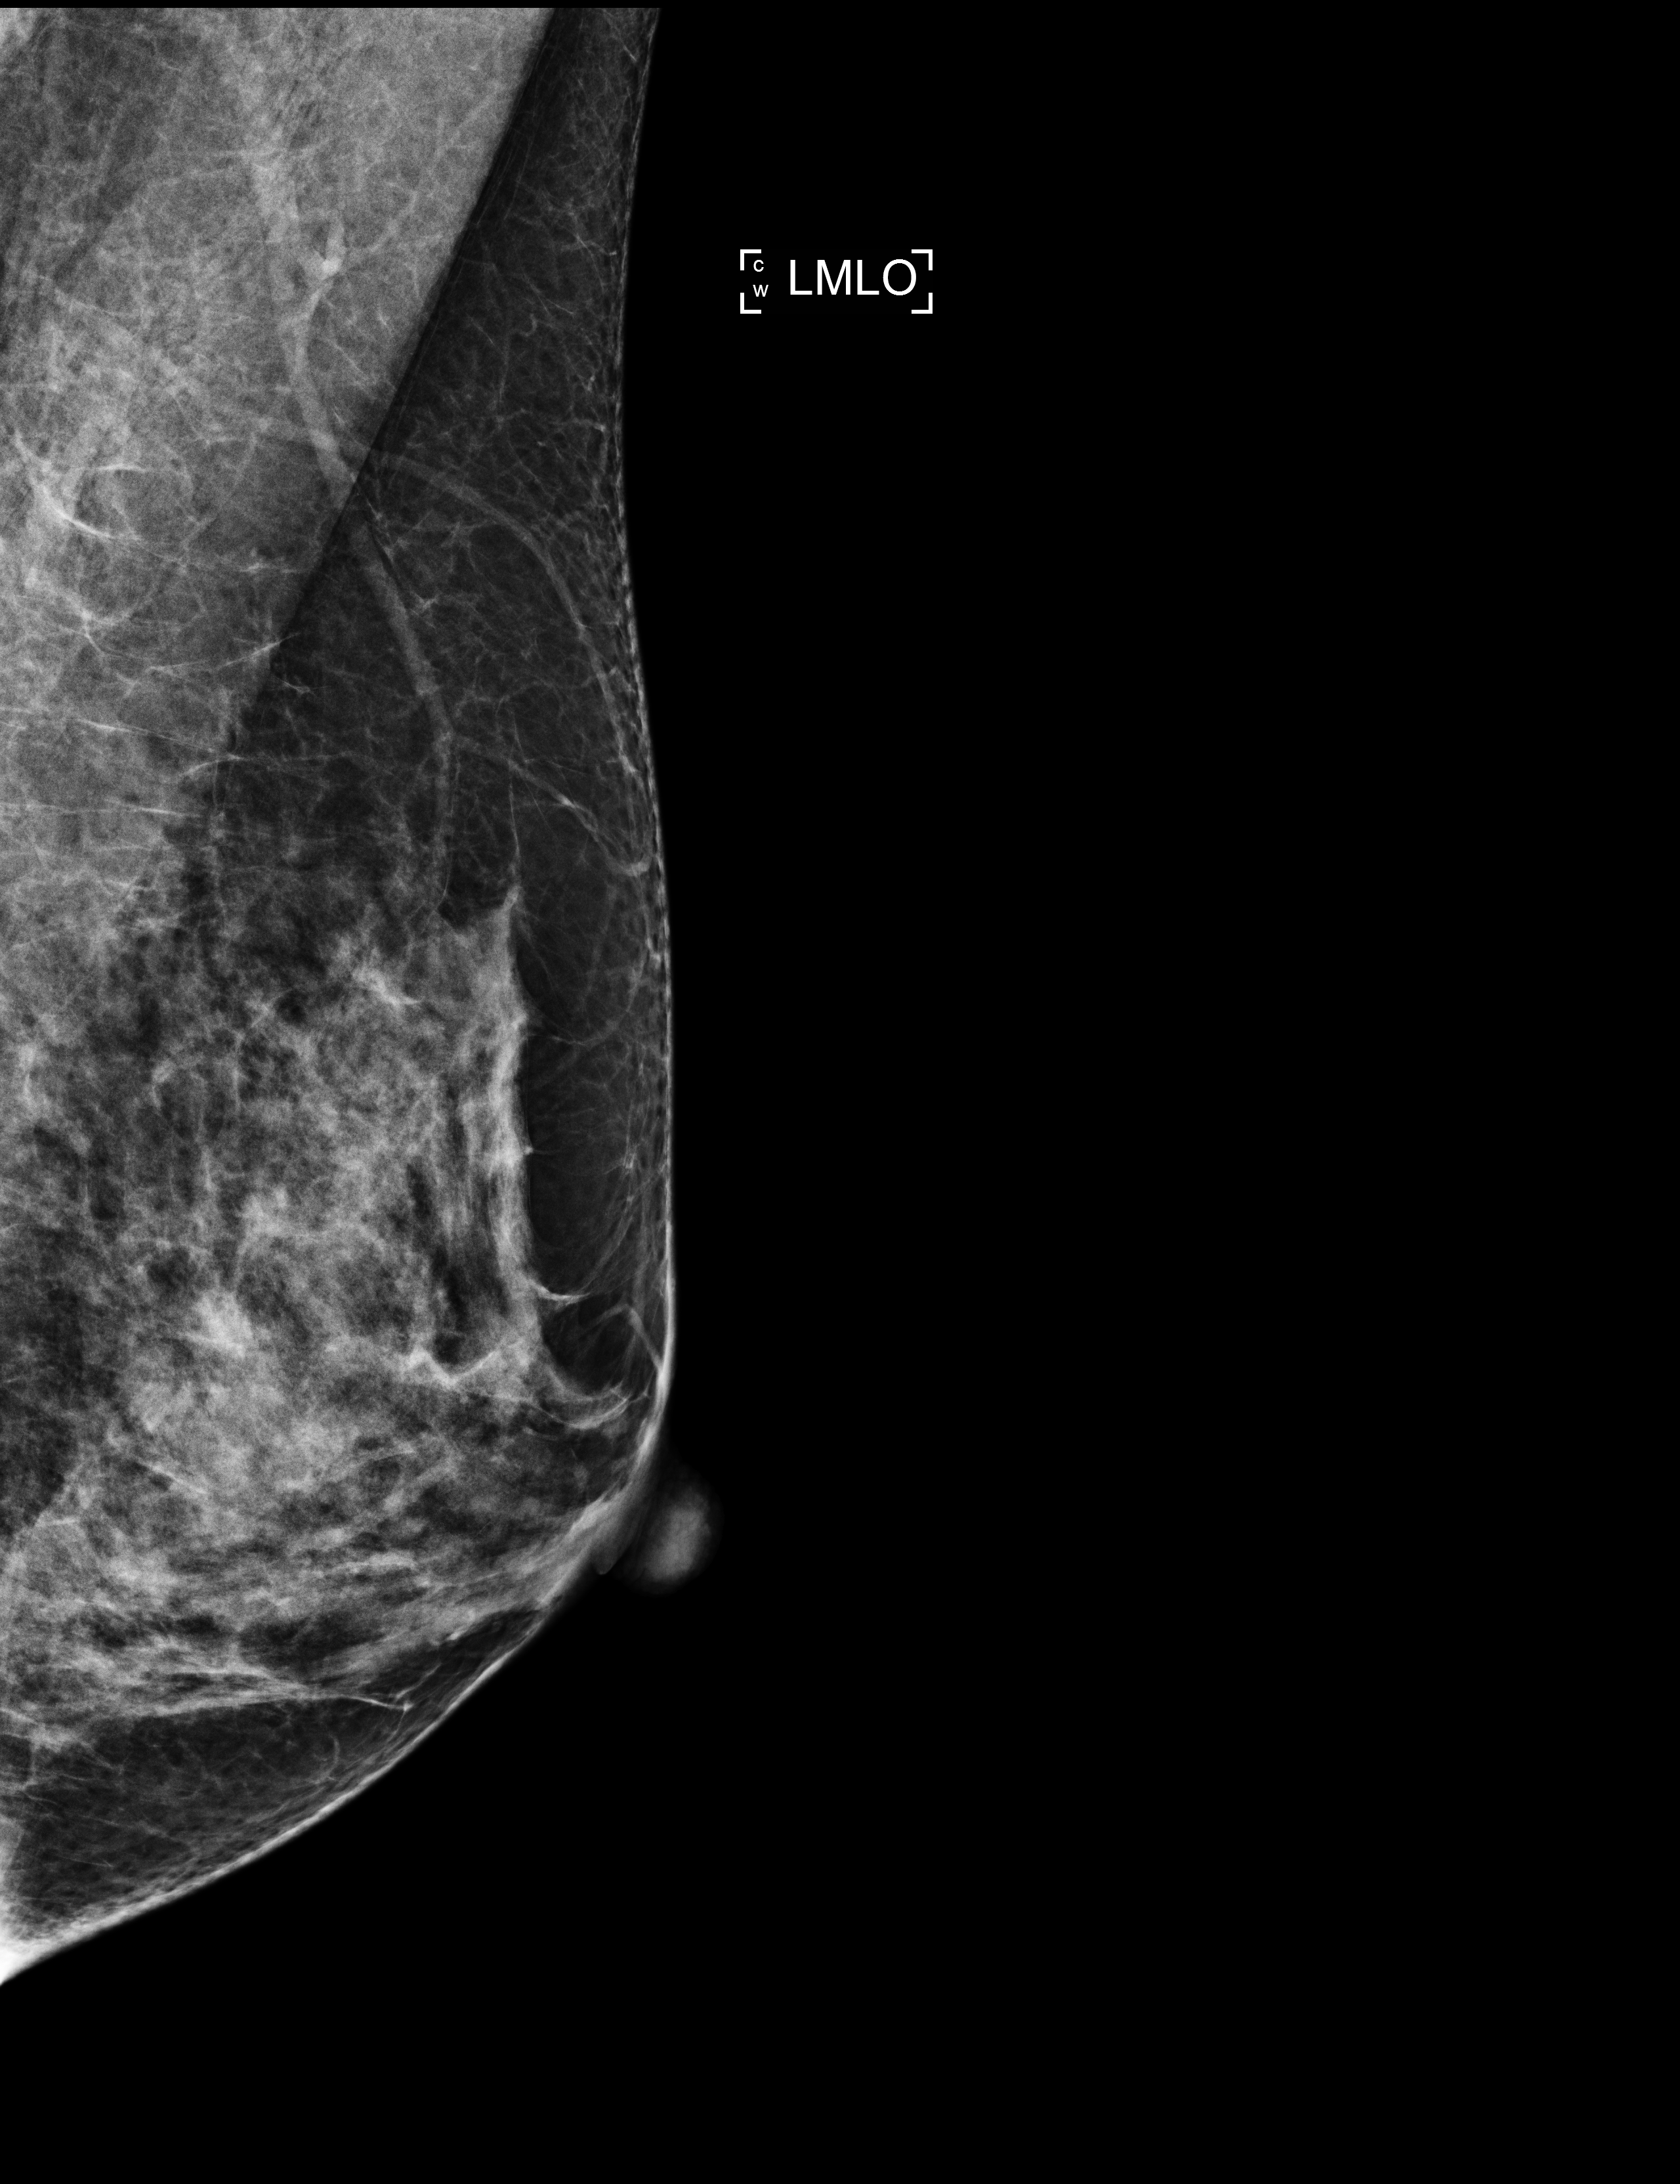
Digital mammogram (FFDM), left breast, MLO view, screening examination, compressed breast thickness 56 mm. Female patient, age 41 years.
- breast density at the screening exam (both breasts): extremely dense (BI-RADS density category d)
- final BI-RADS assessment for this screening round (tomosynthesis exam, both breasts): category 1
- recall: no recall after this screen